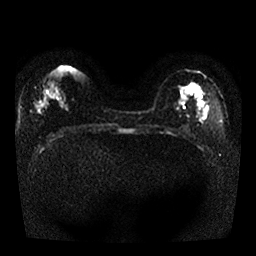
Breast MRI, one axial slice. Diffusion-weighted series; image 2 of 4 stored at this slice position (different b-values; order by instance number). 1.5 T. 4 mm slice thickness. 256 × 256 image matrix. Female patient.
Outlined on this slice (outlined manually by an expert reader):
- tumour on diffusion-weighted imaging: bounding box [x1, y1, x2, y2] px = [195, 85, 199, 92]